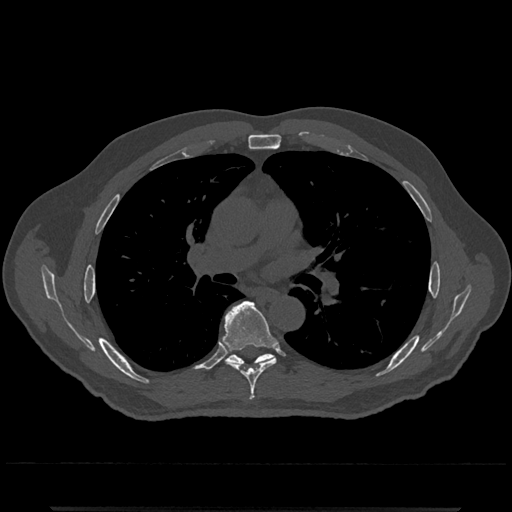
CT including the spine, one axial slice. Slice 756 of 797 in the series (ordered by position). Bone window (W 1800 / L 400 HU). 0.5 mm slice thickness. 512 × 512 image matrix. Patient: male, 67 years. Case-level facts recorded for this patient, not image findings: primary cancer: prostate.
Structures marked on this image (semi-automatic segmentation, software-assisted and operator-edited):
- T6 vertebra: bounding box (x1, y1, x2, y2) in pixels: (223, 301, 276, 400)
- T7 vertebra: (227, 353, 273, 365)